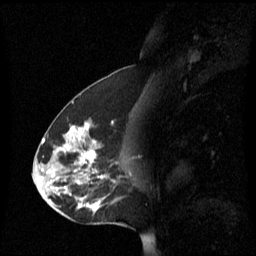
Breast MRI (dynamic contrast-enhanced), one sagittal slice; slice 30 of 60 in the series (ordered by position); dynamic contrast-enhanced series, image 2 of 3 at this slice position (ordered by acquisition); 1.5 T; TE 4.2 ms, TR 8.4 ms; 2.2 mm slice thickness; 256 × 256 image matrix. Patient: female, 45 years. Case-level facts recorded for this patient, not image findings: setting: breast cancer imaged before/during neoadjuvant chemotherapy; receptor status: HR-positive, HER2-negative.
Structures marked on this image (semi-automatic segmentation, software-assisted and operator-edited):
- analysis volume of interest (the breast-tissue region the enhancement analysis was run in; not a lesion): bounding box [x1, y1, x2, y2] px = [38, 122, 129, 221]
- tumour enhancement mask (voxels above the 70 % enhancement threshold inside the analysis volume of interest): [56, 124, 105, 211]